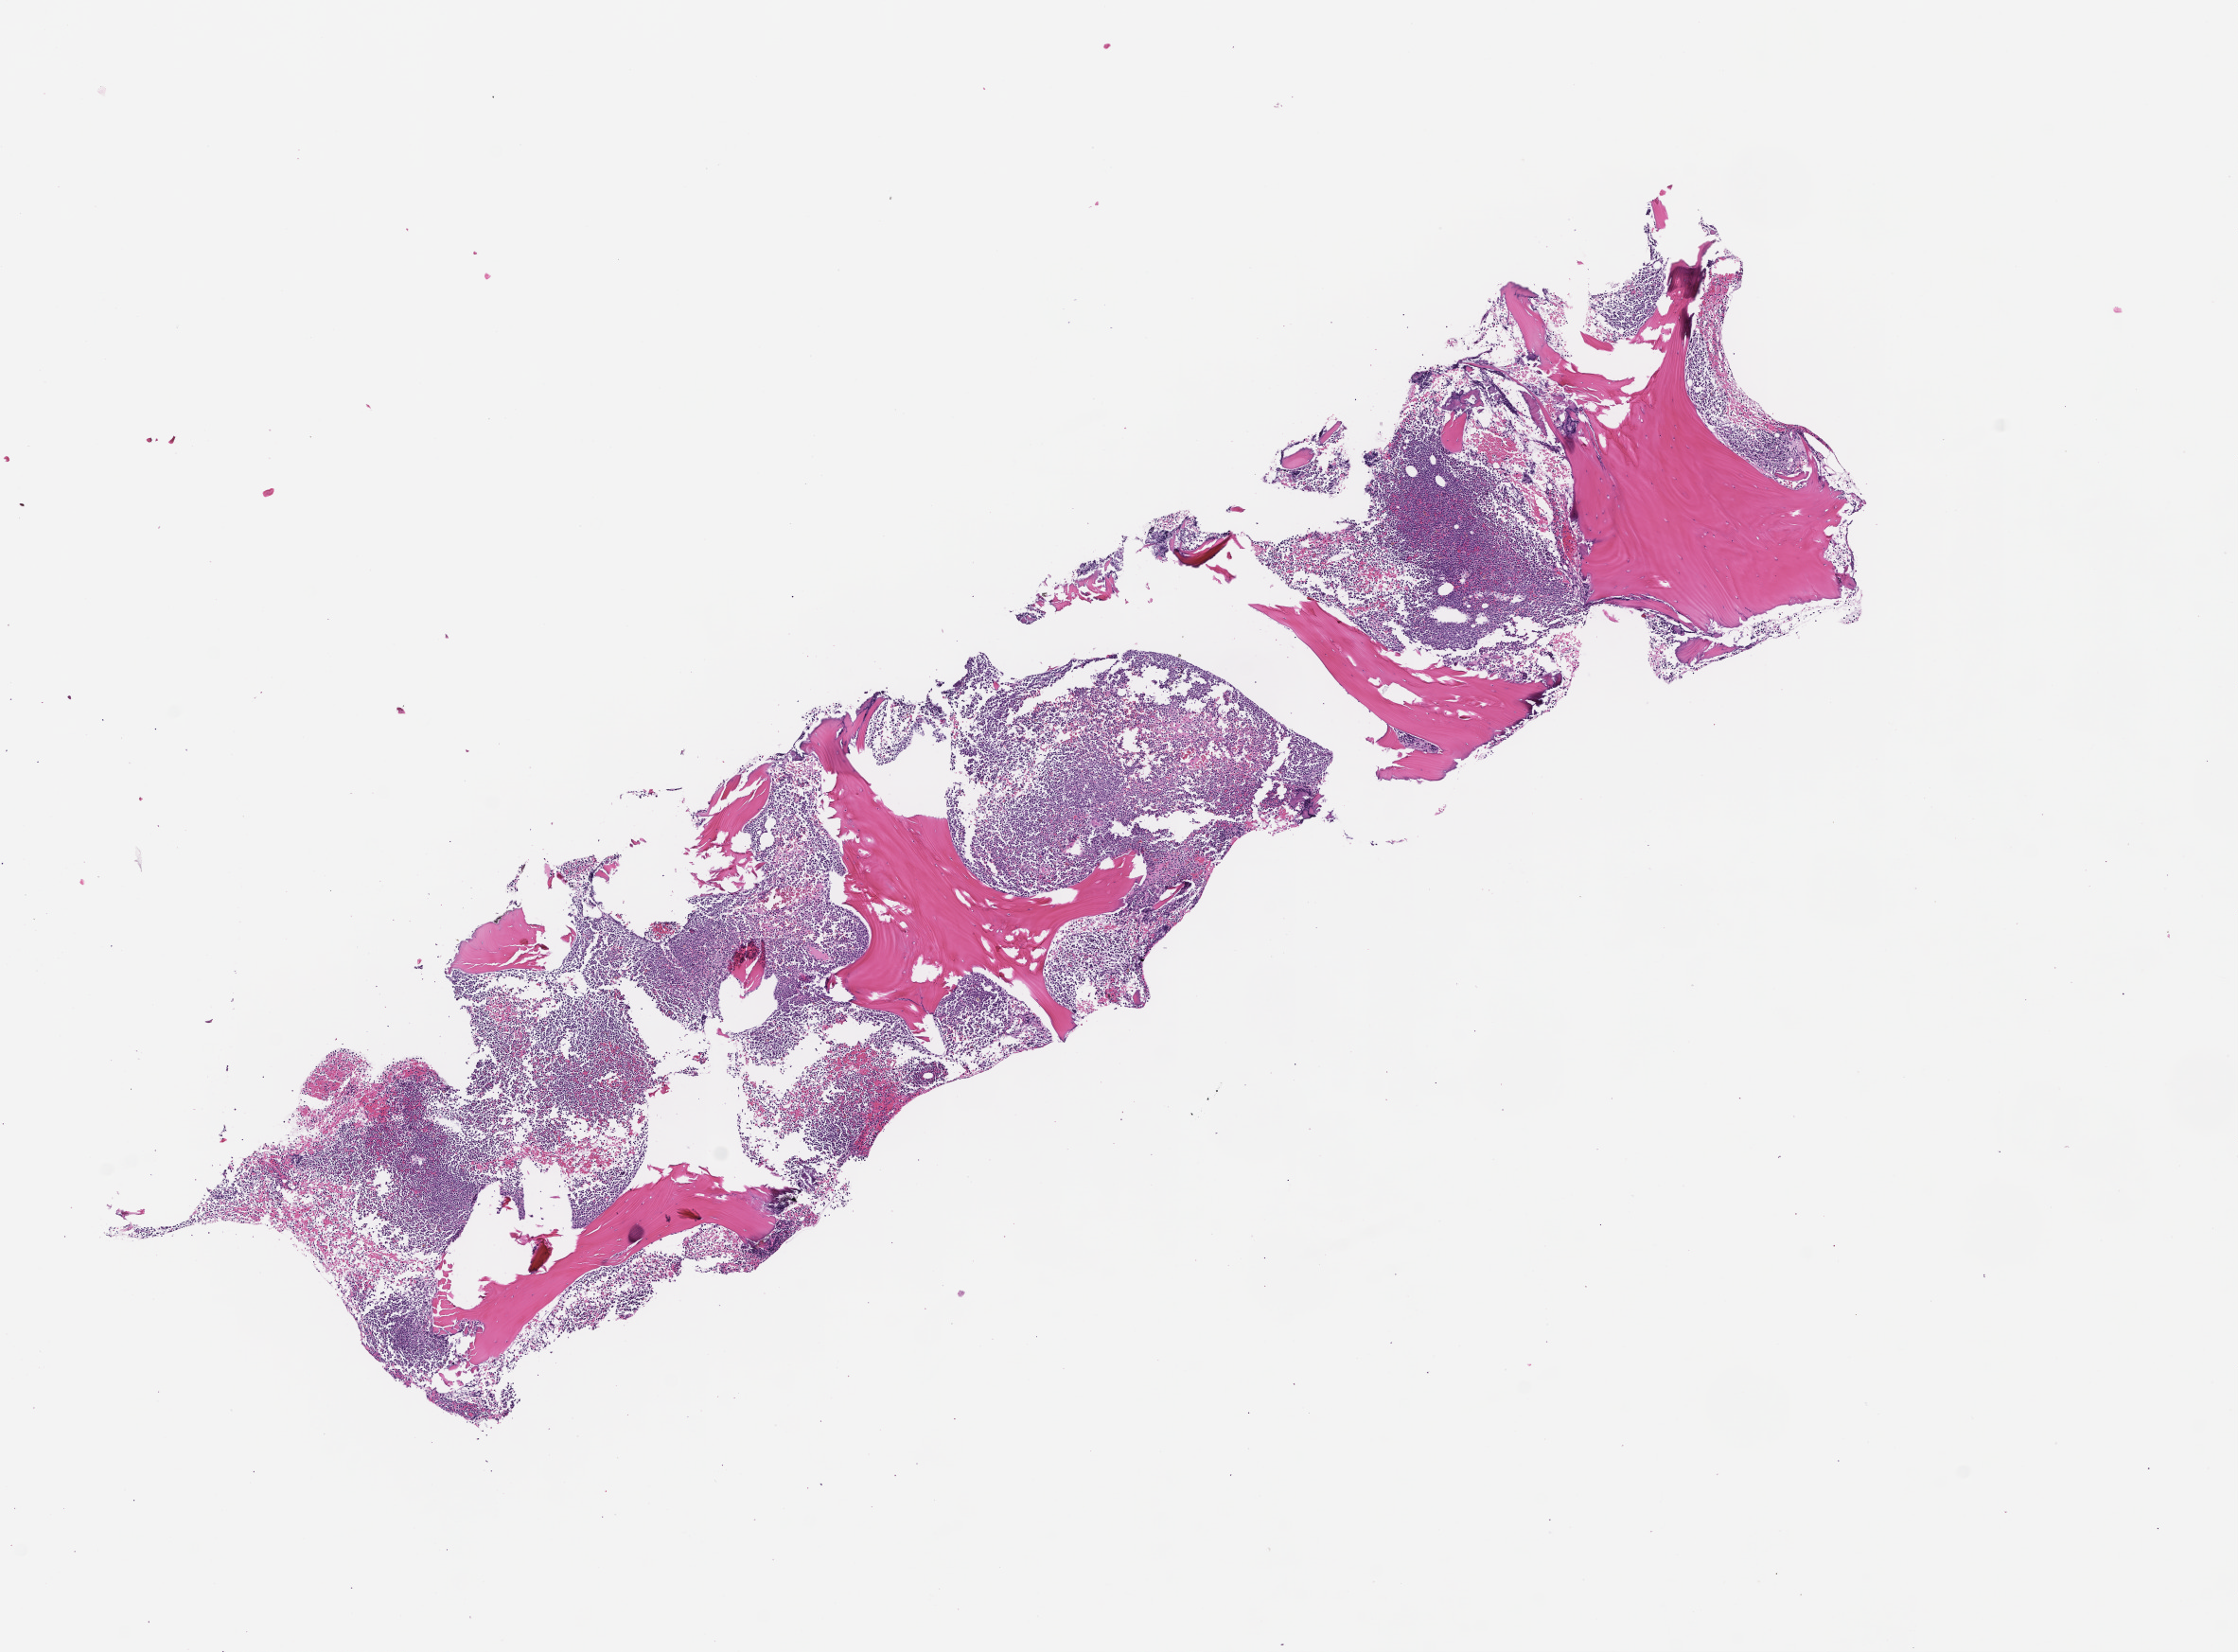
H&E whole-slide image, whole scanned area (about 9.5 x 7.0 mm) shown as a low-resolution overview, formalin-fixed, paraffin-embedded (FFPE) tissue, tissue site: bone marrow, specimen time point: collected at baseline (before treatment). Female patient.
This section: primary tumour tissue. Diagnosis: Acute Myeloid Leukemia Not Otherwise Specified.